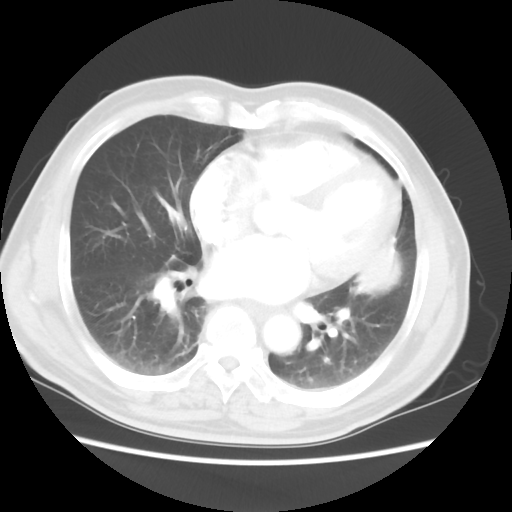
Chest CT, one axial slice; slice 20 of 50 in the series (ordered by position); lung window (W 1500 / L -600 HU); 5 mm slice thickness; 512 × 512 image matrix, field of view 360 × 360 mm. Patient: male, 69 years. From the clinical record (not read from this slice): clinical TNM (as recorded): T3 N1 M1a.
Annotated regions visible in this slice (bounding box drawn by a radiologist):
- lung tumour (recorded histology: squamous cell carcinoma): box from (x=339, y=227) to (x=407, y=320) px